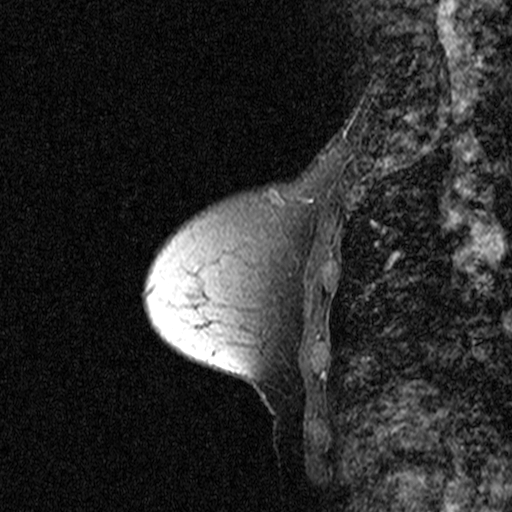
Breast MRI (dynamic contrast-enhanced), one sagittal slice. Slice 17 of 44 in the series (ordered by position). Dynamic contrast-enhanced study with each time point stored as its own series, time point 2 of 3 at this slice position (early post-contrast, ordered by acquisition time). 1.5 T. TE 4.5 ms, TR 11 ms. 2.27 mm slice thickness. 512 × 512 image matrix, field of view 200 × 200 mm. Patient: female, 53 years. Case-level facts recorded for this patient, not image findings: setting: breast cancer imaged before/during neoadjuvant chemotherapy; receptor status: HR-positive, HER2-negative.
Annotated regions visible in this slice (semi-automatic segmentation, software-assisted and operator-edited):
- analysis volume of interest (the breast-tissue region the enhancement analysis was run in; not a lesion): bounding box [x1, y1, x2, y2] px = [200, 178, 317, 309]
- tumour enhancement mask (voxels above the 90 % enhancement threshold inside the analysis volume of interest): [270, 189, 313, 204]